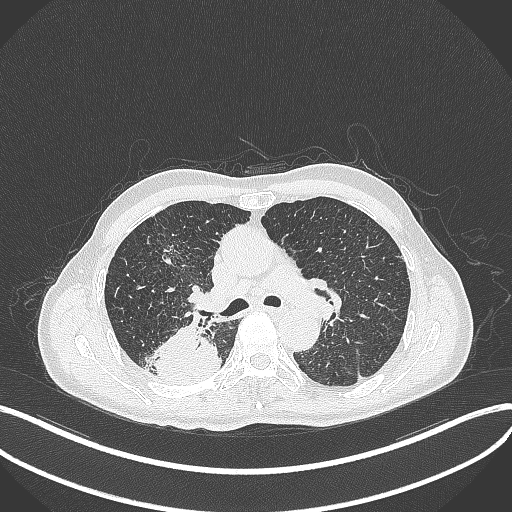
Chest CT, one axial slice. Position 291 of 428 along the scan axis. 120 kVp. Lung window (W 1500 / L -600 HU). 1 mm slice thickness. 512 × 512 image matrix, field of view 400 × 400 mm. Male patient, age 79 years. From the clinical record (not read from this slice): clinical TNM (as recorded): T3 N0 M0.
Structures marked on this image (bounding box drawn by a radiologist):
- lung tumour (recorded histology: adenocarcinoma): bounding box [x1, y1, x2, y2] px = [149, 324, 222, 383]